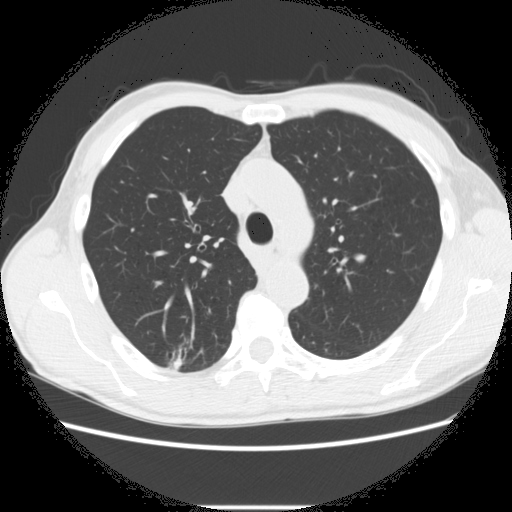
Axial slice from a low-dose chest CT screening exam. Second annual screen. Lung window (W 1500 / L -600 HU). 2.5 mm slice thickness. 120 kVp. Slice 82 of 282 in the series. Male, age 66 years at enrolment. Former smoker at enrolment.
• Lesion marked by an expert reader, bounding box <163,340,221,379> (left, top, right, bottom; pixels).
• The screening reader recorded 5 non-calcified nodules or masses ≥4 mm on this exam (right lower lobe, right upper lobe, right upper lobe, right upper lobe, left lower lobe); which of them this box marks is not recorded.
• Official screen result: positive, change unspecified: nodule(s) >= 4 mm or enlarging nodule(s), mass(es), or other non-specific abnormalities suspicious for lung cancer.
• Later outcome: lung cancer diagnosed 75 days after this screen — adenocarcinoma, NOS, right upper lobe, undifferentiated (G4), stage IA (AJCC 6th edition), 20 mm at pathology.